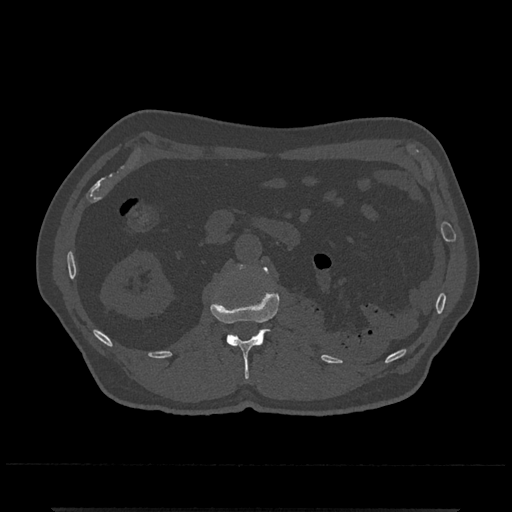
CT including the spine, one axial slice; bone window (W 1800 / L 400 HU); 0.5 mm slice thickness; 512 × 512 image matrix, field of view 393 × 393 mm. Male patient, age 67 years. Case-level facts recorded for this patient, not image findings: primary cancer: prostate.
Annotated regions visible in this slice (semi-automatically segmented with operator editing):
- L1 vertebra: bounding box [x1, y1, x2, y2] px = [211, 267, 280, 379]
- L2 vertebra: [237, 264, 245, 269]